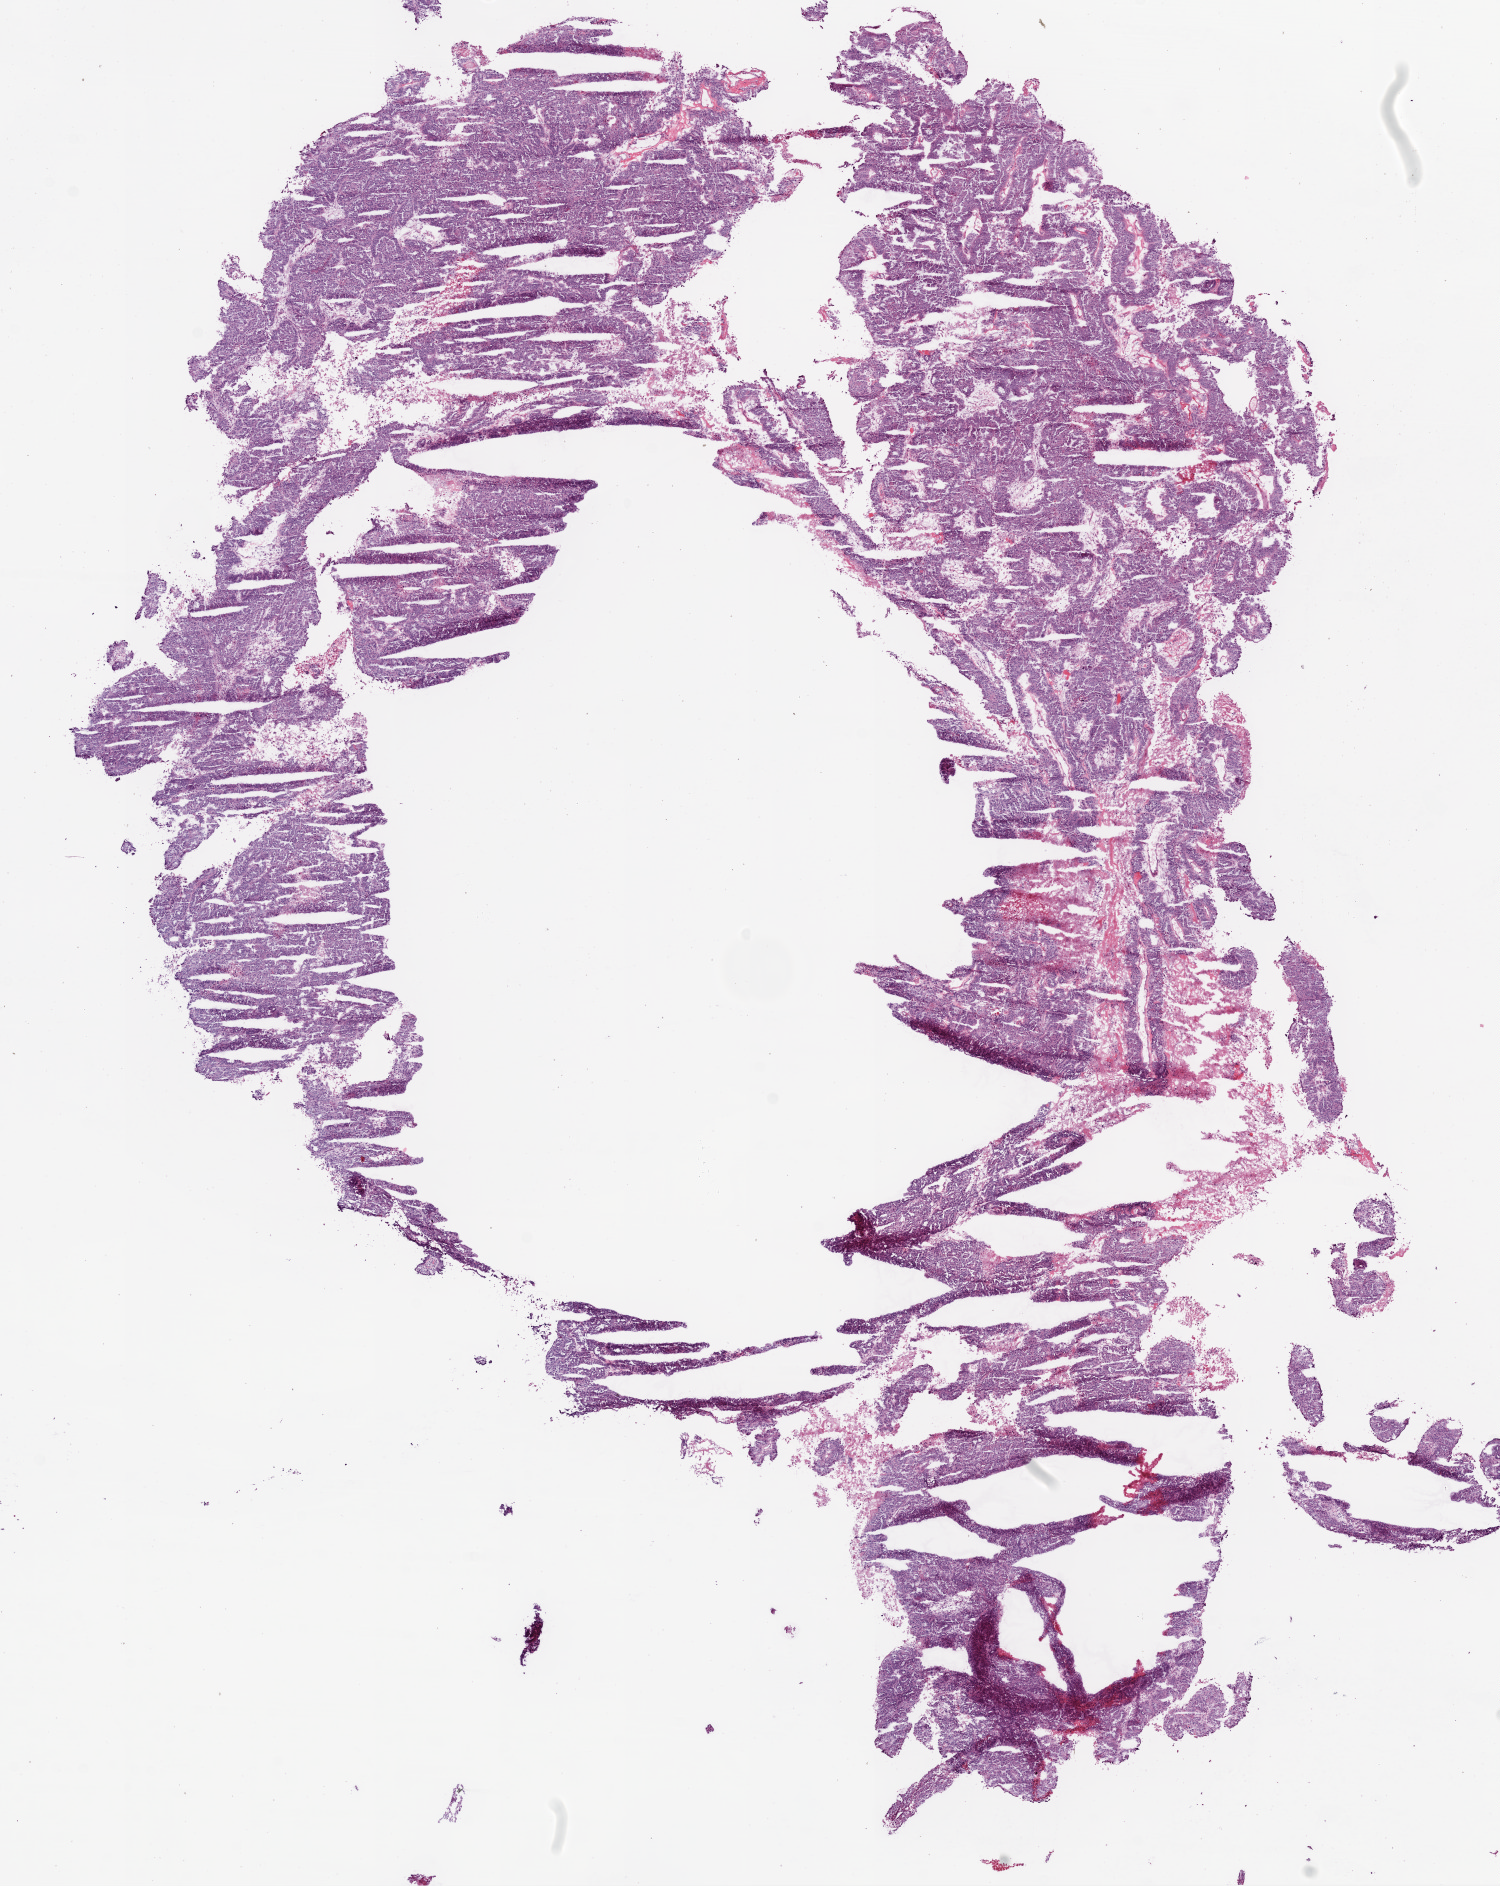
H&E whole-slide image — shown as a low-resolution overview of the whole scanned area (about 12.0 x 15.1 mm); frozen section from the bottom of the tissue portion; sample: primary tumour, ovary. Female patient; age at initial diagnosis 52 years. Histologic grade: G3 (poorly differentiated). Composition of this section per pathologist review: tumour cells 85%, tumour nuclei 90%, normal cells 0%, stromal cells 10%, necrosis 5%.
* histologic diagnosis: Serous cystadenocarcinoma, NOS
* FIGO stage: IIIC